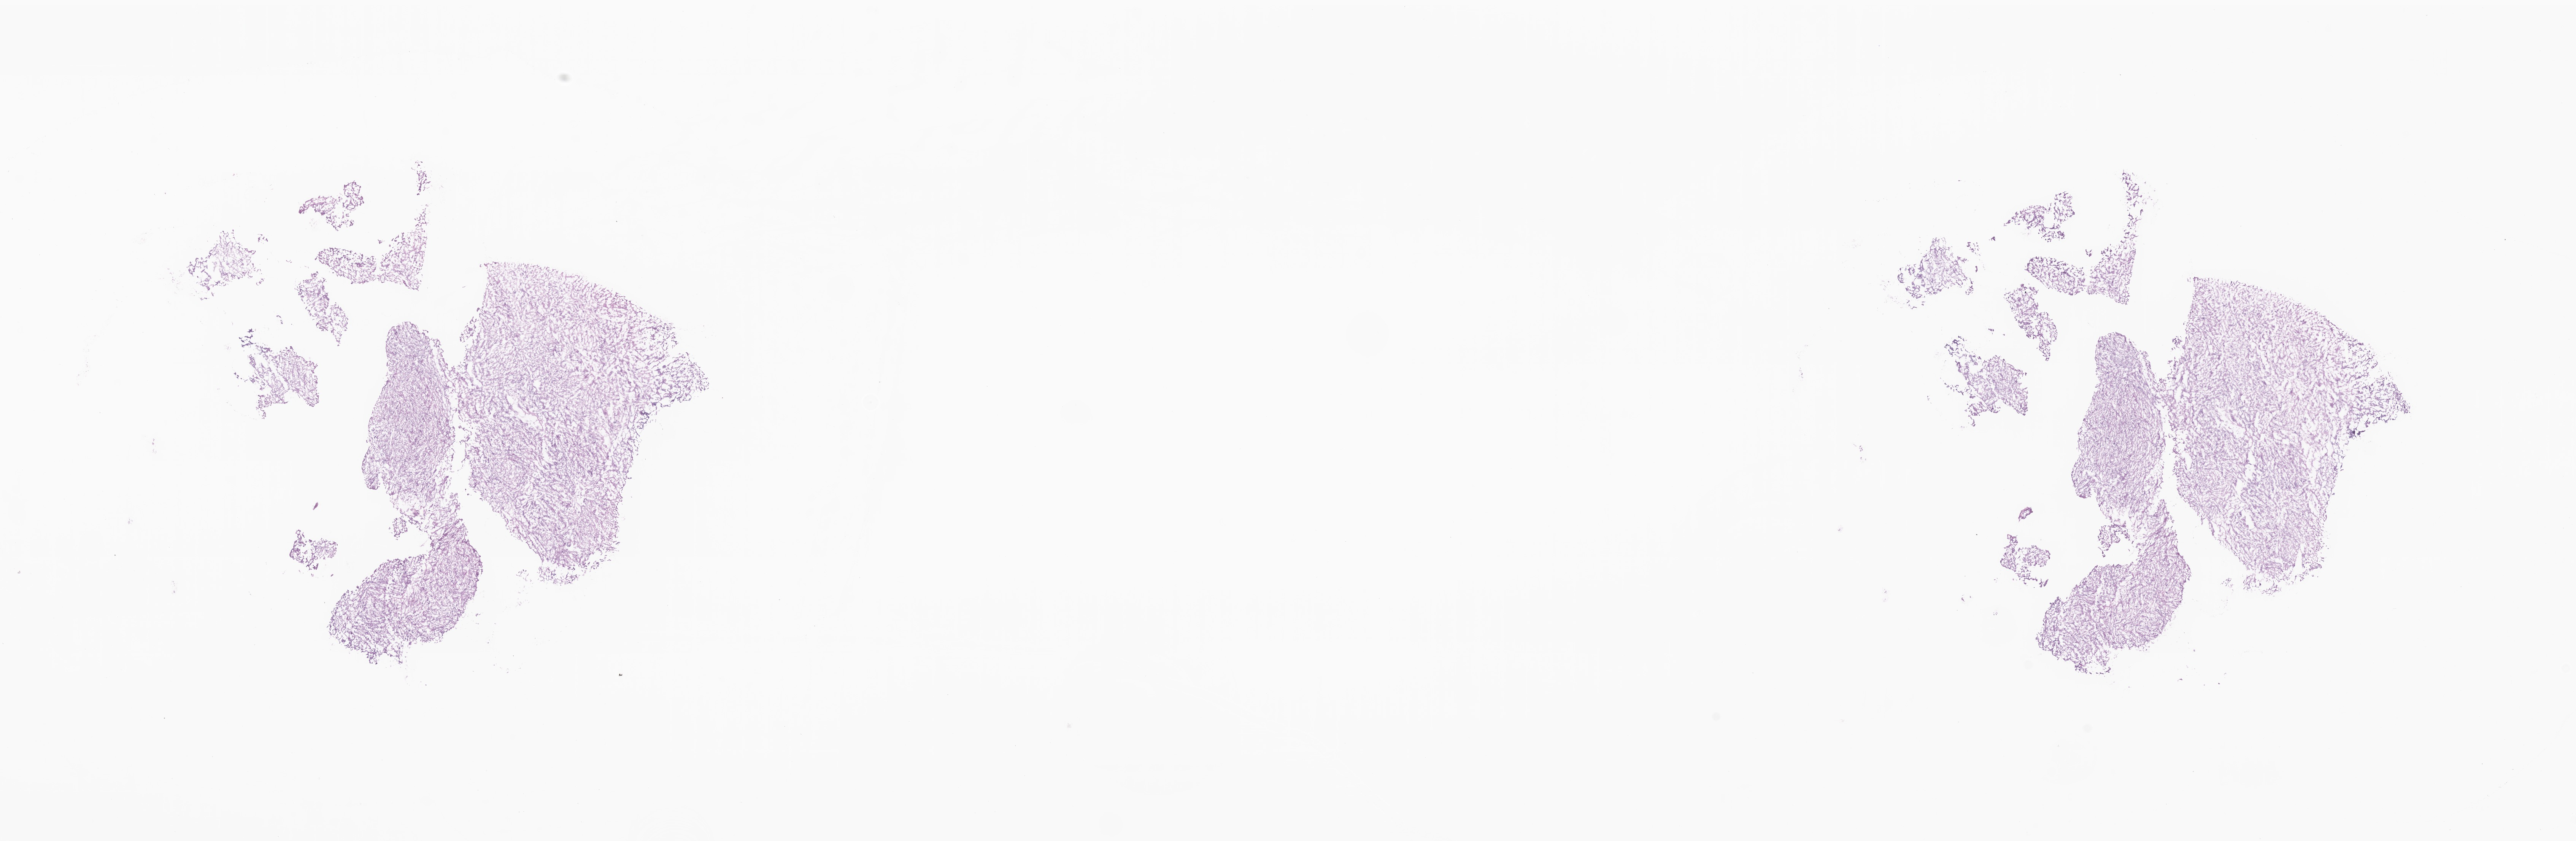
Digitized hematoxylin and eosin (H&E)-stained section, whole scanned area (about 28.6 x 9.3 mm) shown as a low-resolution overview; cryosection; specimen: metastatic tumor tissue, resected from connective, subcutaneous and other soft tissues. Female, age 45 years at initial diagnosis. Pathologist review of this section (percent, as recorded): tumor cells 90%, tumor nuclei 90%, stromal cells 10%, necrosis 0%, normal cells 0%. Infiltration values recorded for this section: lymphocyte infiltration 0%, monocyte infiltration 0%, neutrophil infiltration 0%.
Patient diagnosis (primary): Leiomyosarcoma, NOS. Section: bottom of the tissue portion.